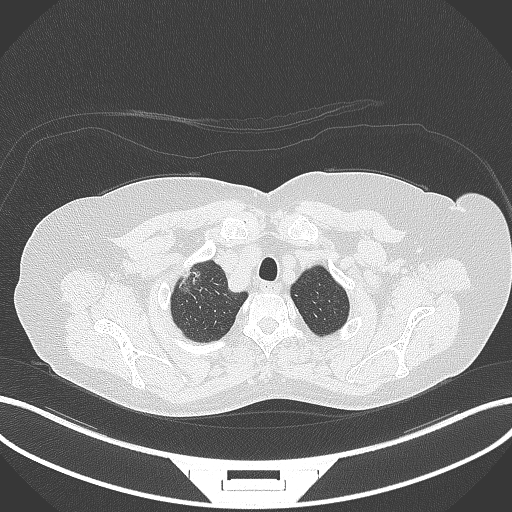
Chest CT, one axial slice; slice 316 of 365 in the series (ordered by position); reconstruction kernel B70f; 120 kVp; lung window (W 1500 / L -600 HU); 1 mm slice thickness; 512 × 512 image matrix, field of view 400 × 400 mm. Patient: female, 62 years. Case-level facts recorded for this patient, not image findings: clinical TNM (as recorded): T1c N0 M0.
Outlined on this slice (bounding box drawn by a radiologist):
- lung tumour (recorded histology: adenocarcinoma): bounding box (x1, y1, x2, y2) in pixels: (179, 262, 207, 300)